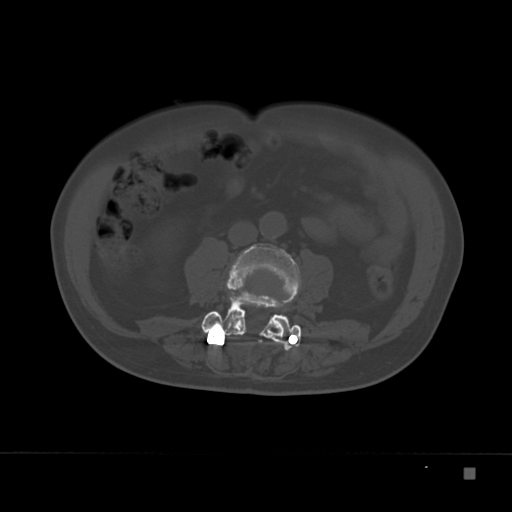
CT including the spine, one axial slice. Slice 56 of 332 in the series (ordered by position). Bone window (W 1800 / L 400 HU). 1.5 mm slice thickness. 512 × 512 image matrix, field of view 389 × 389 mm. Patient: male, 72 years. From the clinical record (not read from this slice): primary cancer: skeletal.
Annotated regions visible in this slice (semi-automatic segmentation, software-assisted and operator-edited):
- L3 vertebra: box from (x=207, y=244) to (x=301, y=331) px
- L4 vertebra: (x=201, y=290)–(x=302, y=348)